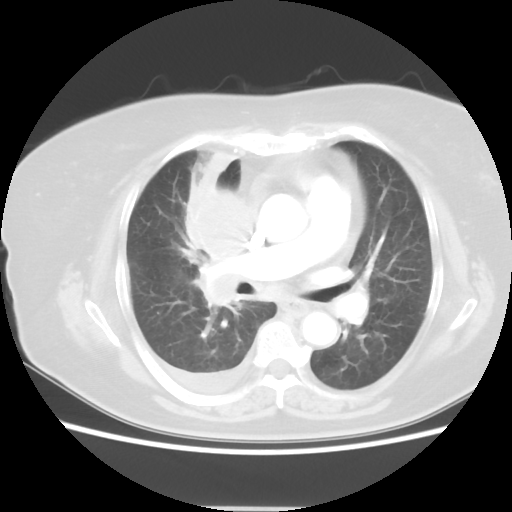
Chest CT, one axial slice; position 27 of 48 along the scan axis; lung window (W 1500 / L -600 HU); 5 mm slice thickness; 512 × 512 image matrix, field of view 360 × 360 mm. Patient: female, 73 years. Case-level facts recorded for this patient, not image findings: clinical TNM (as recorded): T3 N3 M1b.
Outlined on this slice (rectangle marked by the reading radiologist):
- lung tumour (recorded histology: small cell carcinoma): bounding box [x1, y1, x2, y2] px = [178, 147, 270, 313]